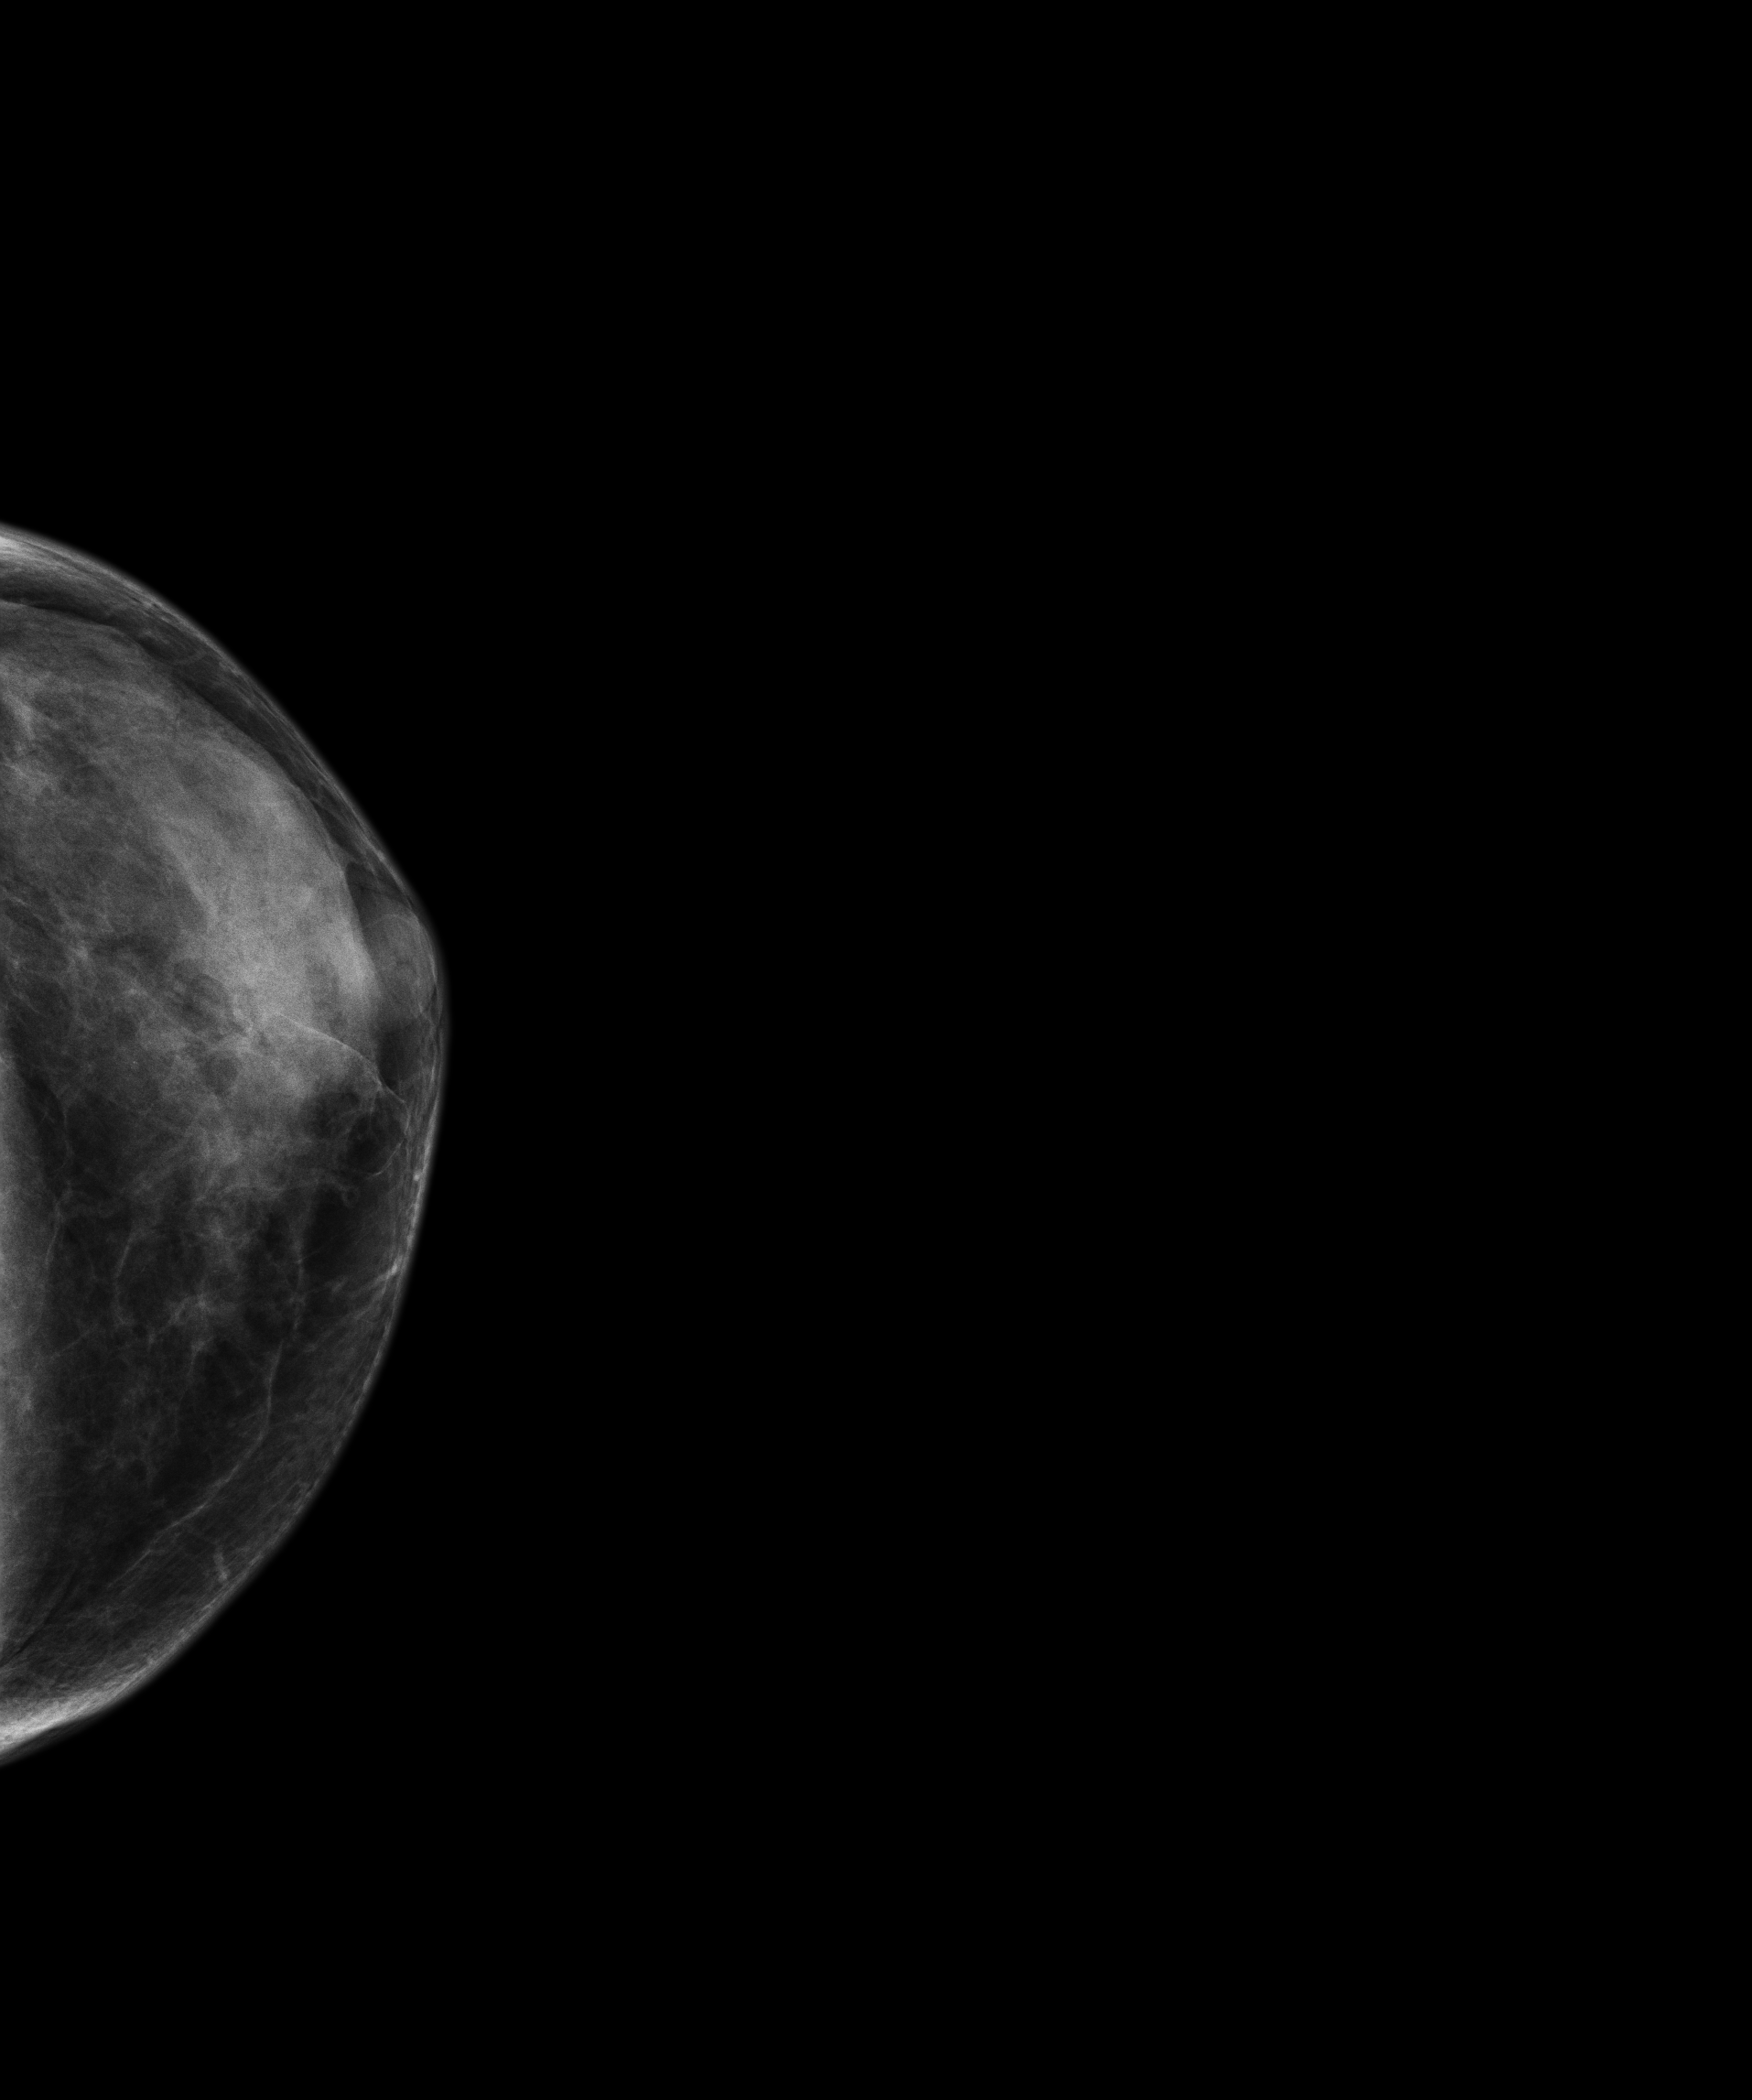
Screening examination, compressed breast thickness 25 mm, system: Senographe Essential ADS_56.21.3. Patient: female, 56 years.
Image type: full-field digital mammogram. Breast: left. Projection: cranio-caudal projection.